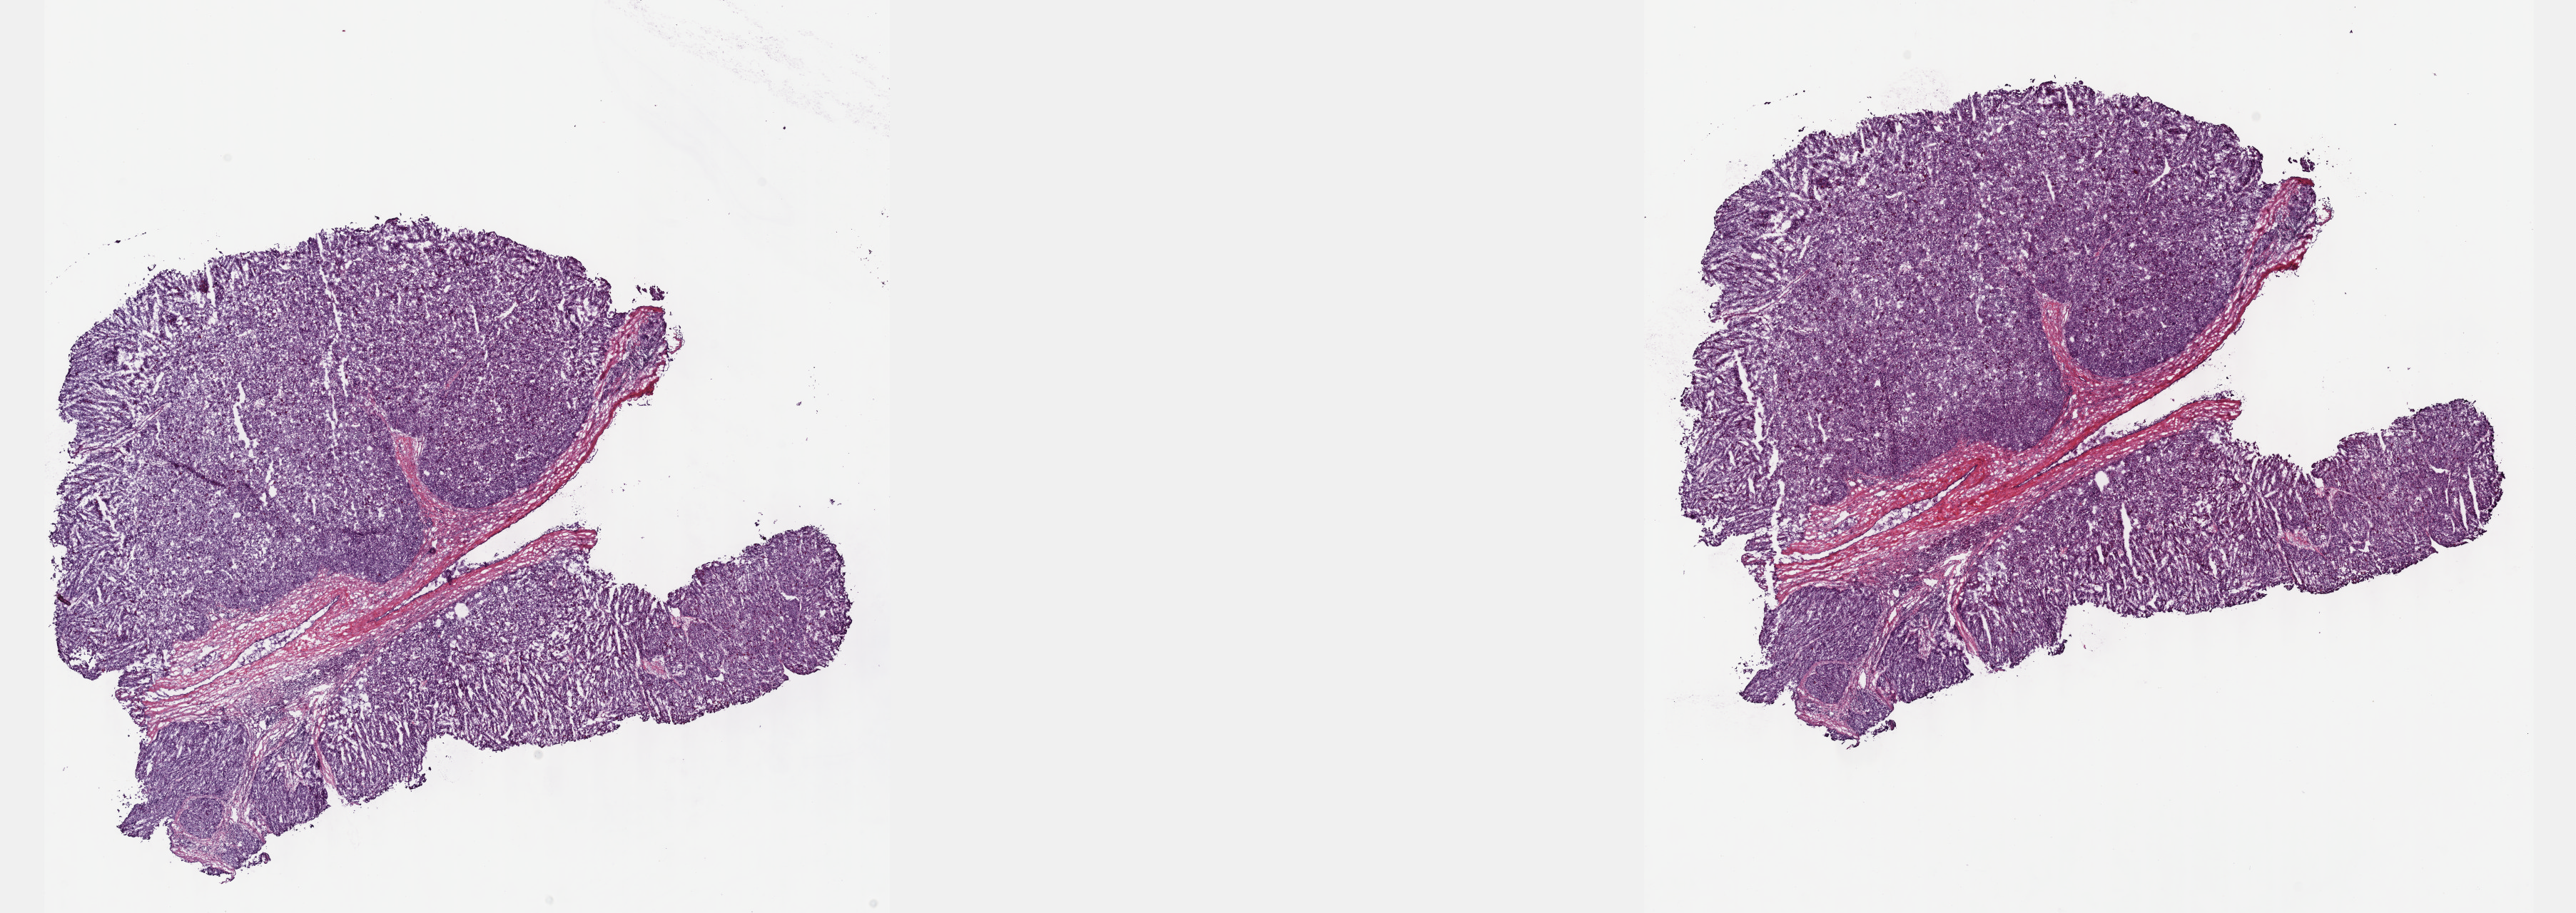
Whole-slide histology image, H&E — whole scanned area (about 29.2 x 10.3 mm) shown as a low-resolution overview. Frozen section from the top of the tissue portion. Liver, primary tumour sample. Male, age 69 years at initial diagnosis. Histologic grade: G3 (poorly differentiated). Pathologist review of this section (percent, as recorded): tumour cells 85%, tumour nuclei 95%, normal cells 0%, stromal cells 15%, necrosis 0%. Infiltration values recorded for this section: lymphocyte infiltration 0%, monocyte infiltration 0%, neutrophil infiltration 0%.
AJCC pathologic stage: II (6th edition). TNM: T2 N0 M0. Histologic diagnosis: Hepatocellular carcinoma, NOS.